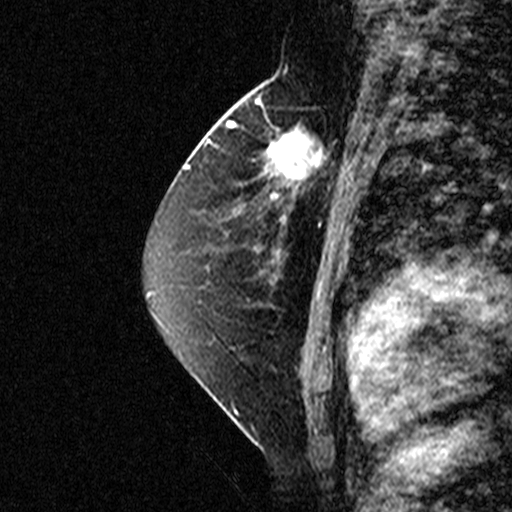
Breast MRI (dynamic contrast-enhanced), one sagittal slice; position 24 of 44 along the scan axis; dynamic contrast-enhanced study with each time point stored as its own series, time point 2 of 3 at this slice position (early post-contrast, ordered by acquisition time); 1.5 T; TE 4.5 ms, TR 11 ms; 3 mm slice thickness; 512 × 512 image matrix, field of view 200 × 200 mm. Female patient, age 49 years. From the clinical record (not read from this slice): setting: breast cancer imaged before/during neoadjuvant chemotherapy; receptor status: triple-negative.
Structures marked on this image (semi-automatically segmented with operator editing):
- analysis volume of interest (the breast-tissue region the enhancement analysis was run in; not a lesion): bounding box <254,112,347,207> (left, top, right, bottom; pixels)
- tumour enhancement mask (voxels above the 90 % enhancement threshold inside the analysis volume of interest): <254,112,347,207>